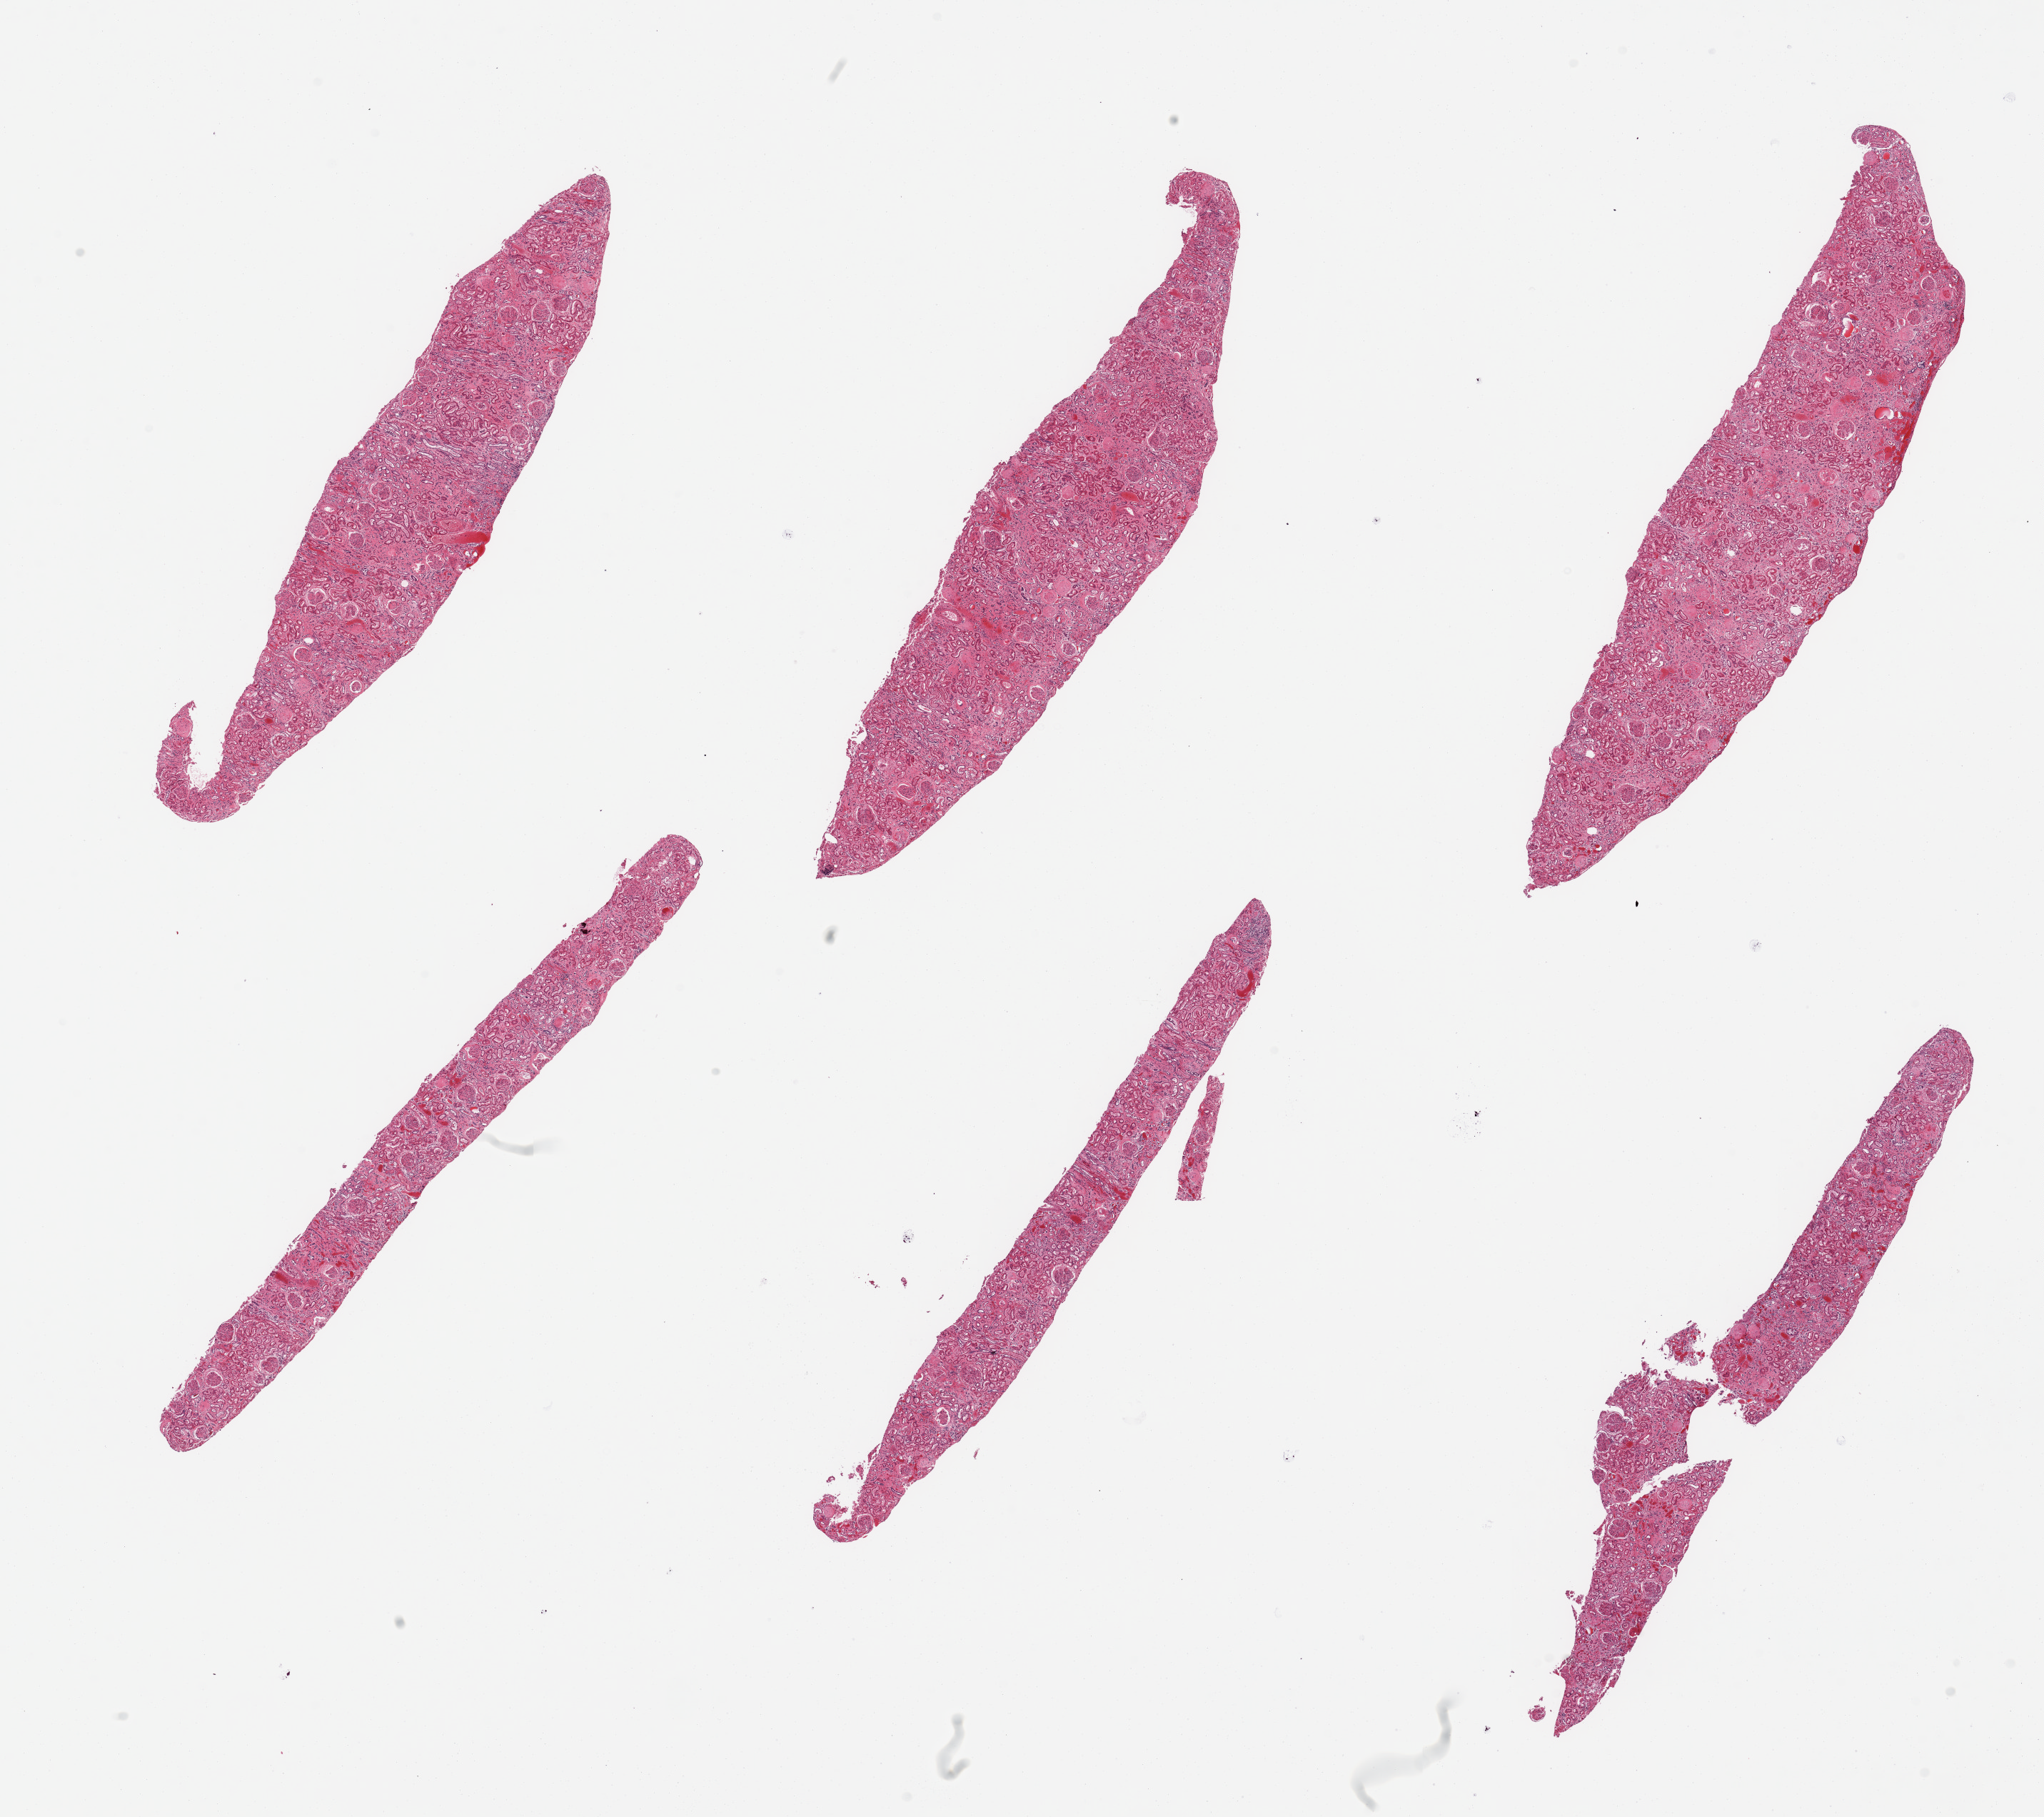
Digitized haematoxylin and eosin-stained section, low-resolution overview of the scanned area, about 22.6 x 20.1 mm; PAXgene-fixed paraffin-embedded (PFPE) section; sampled site (target tissue): renal cortex; tissue donor sample. Donor: male.
Review note (as recorded): 6 pieces, glomeruli present, prominent mesangial thickening, suggests diabetic effect. Tubules with marked autolysis.